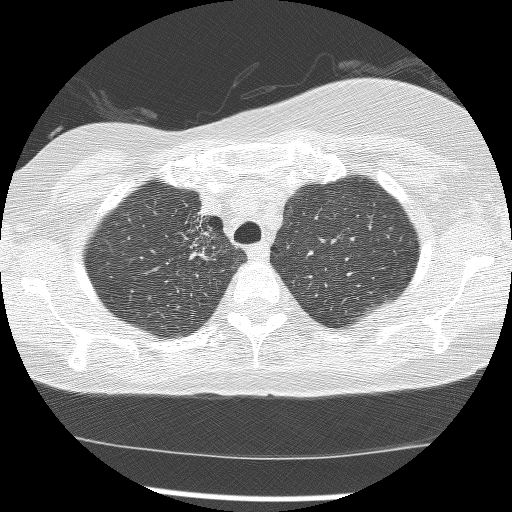
Low-dose screening chest CT, axial slice, baseline screening round, lung window (W 1500 / L -600 HU), 2.5 mm slice thickness, slice 33 of 172 in the series, 512 × 512 image matrix. Female participant, aged 56 years at enrolment. Current smoker at enrolment.
Expert reader's lesion annotation, bounding box [x1, y1, x2, y2] px = [166, 206, 225, 277]. The screening reader recorded 2 non-calcified nodules or masses ≥4 mm on this exam; which of them this box marks is not recorded. Official screen result: positive, change unspecified: nodule(s) >= 4 mm or enlarging nodule(s), mass(es), or other non-specific abnormalities suspicious for lung cancer.